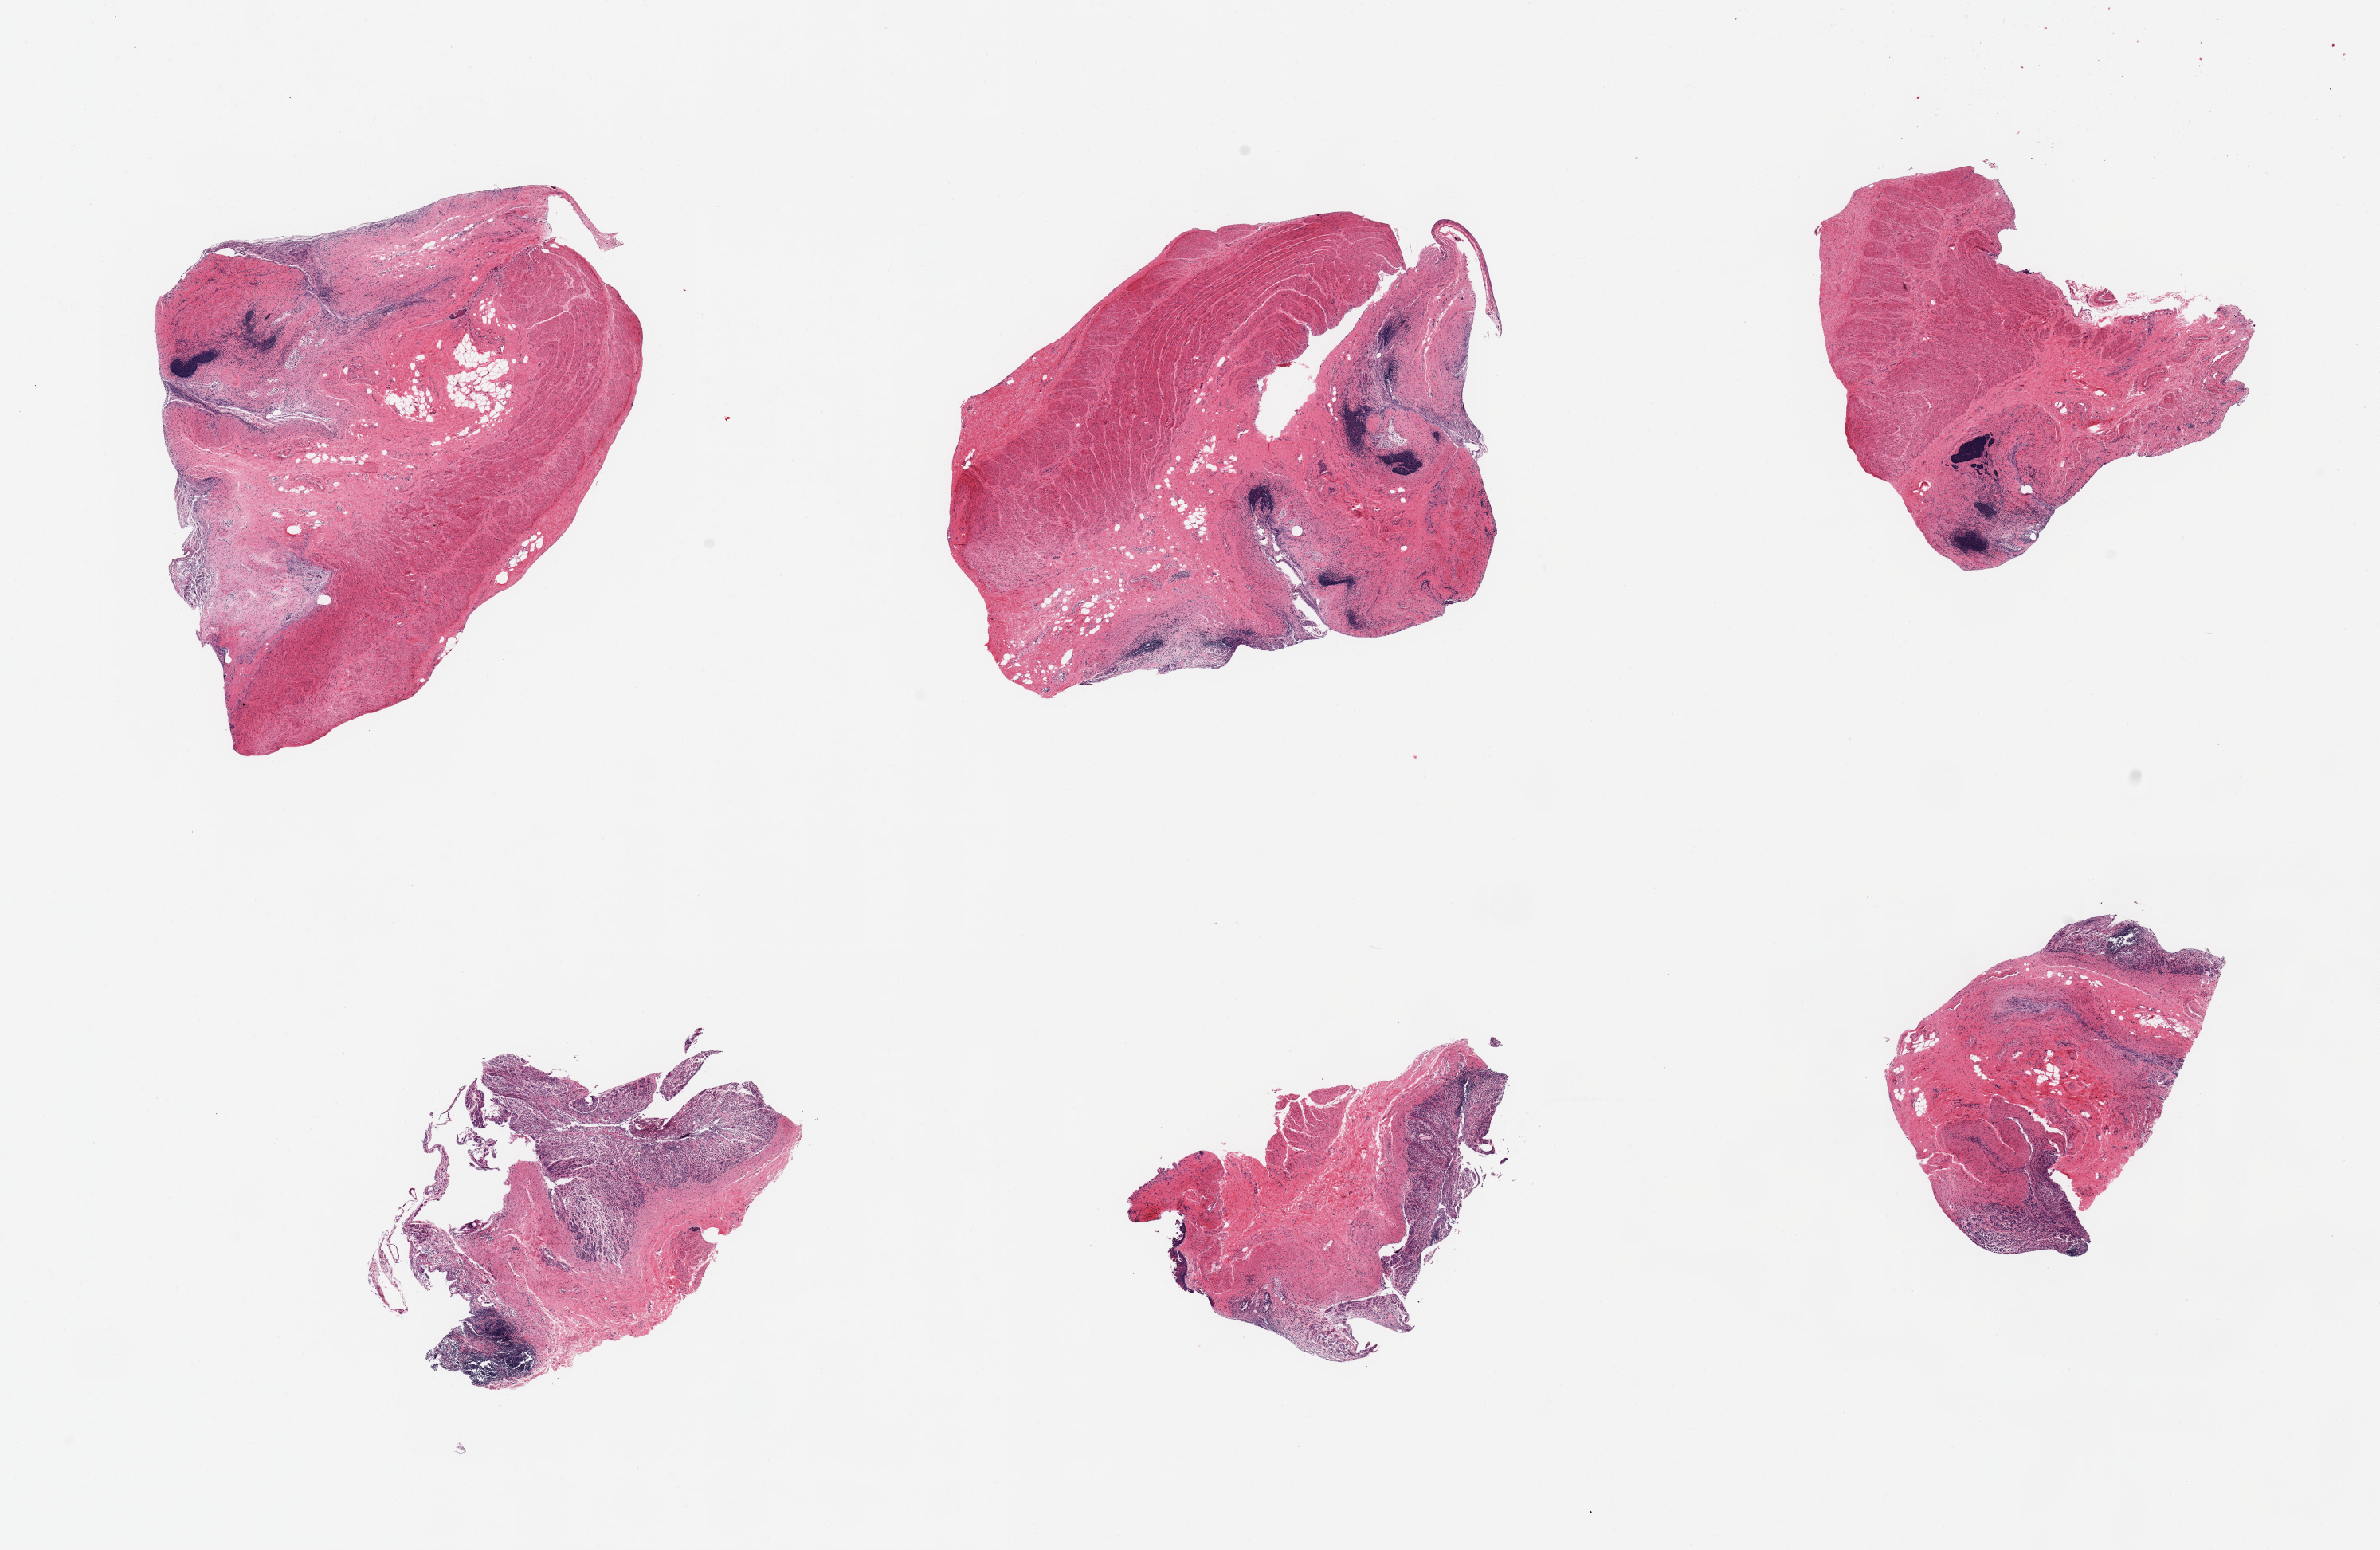
Digitized haematoxylin and eosin-stained section — whole scanned area (about 23.6 x 15.4 mm, acquisition: 20x scan) shown as a low-resolution overview, PAXgene-fixed paraffin-embedded (PFPE) section, section of gastroesophageal junction (target tissue), tissue donor sample. Donor sex: female.
Review note (as recorded): 6 pieces; muscularis with significant residual autolyzed mucosa (squamous/gastric) and inflammation.